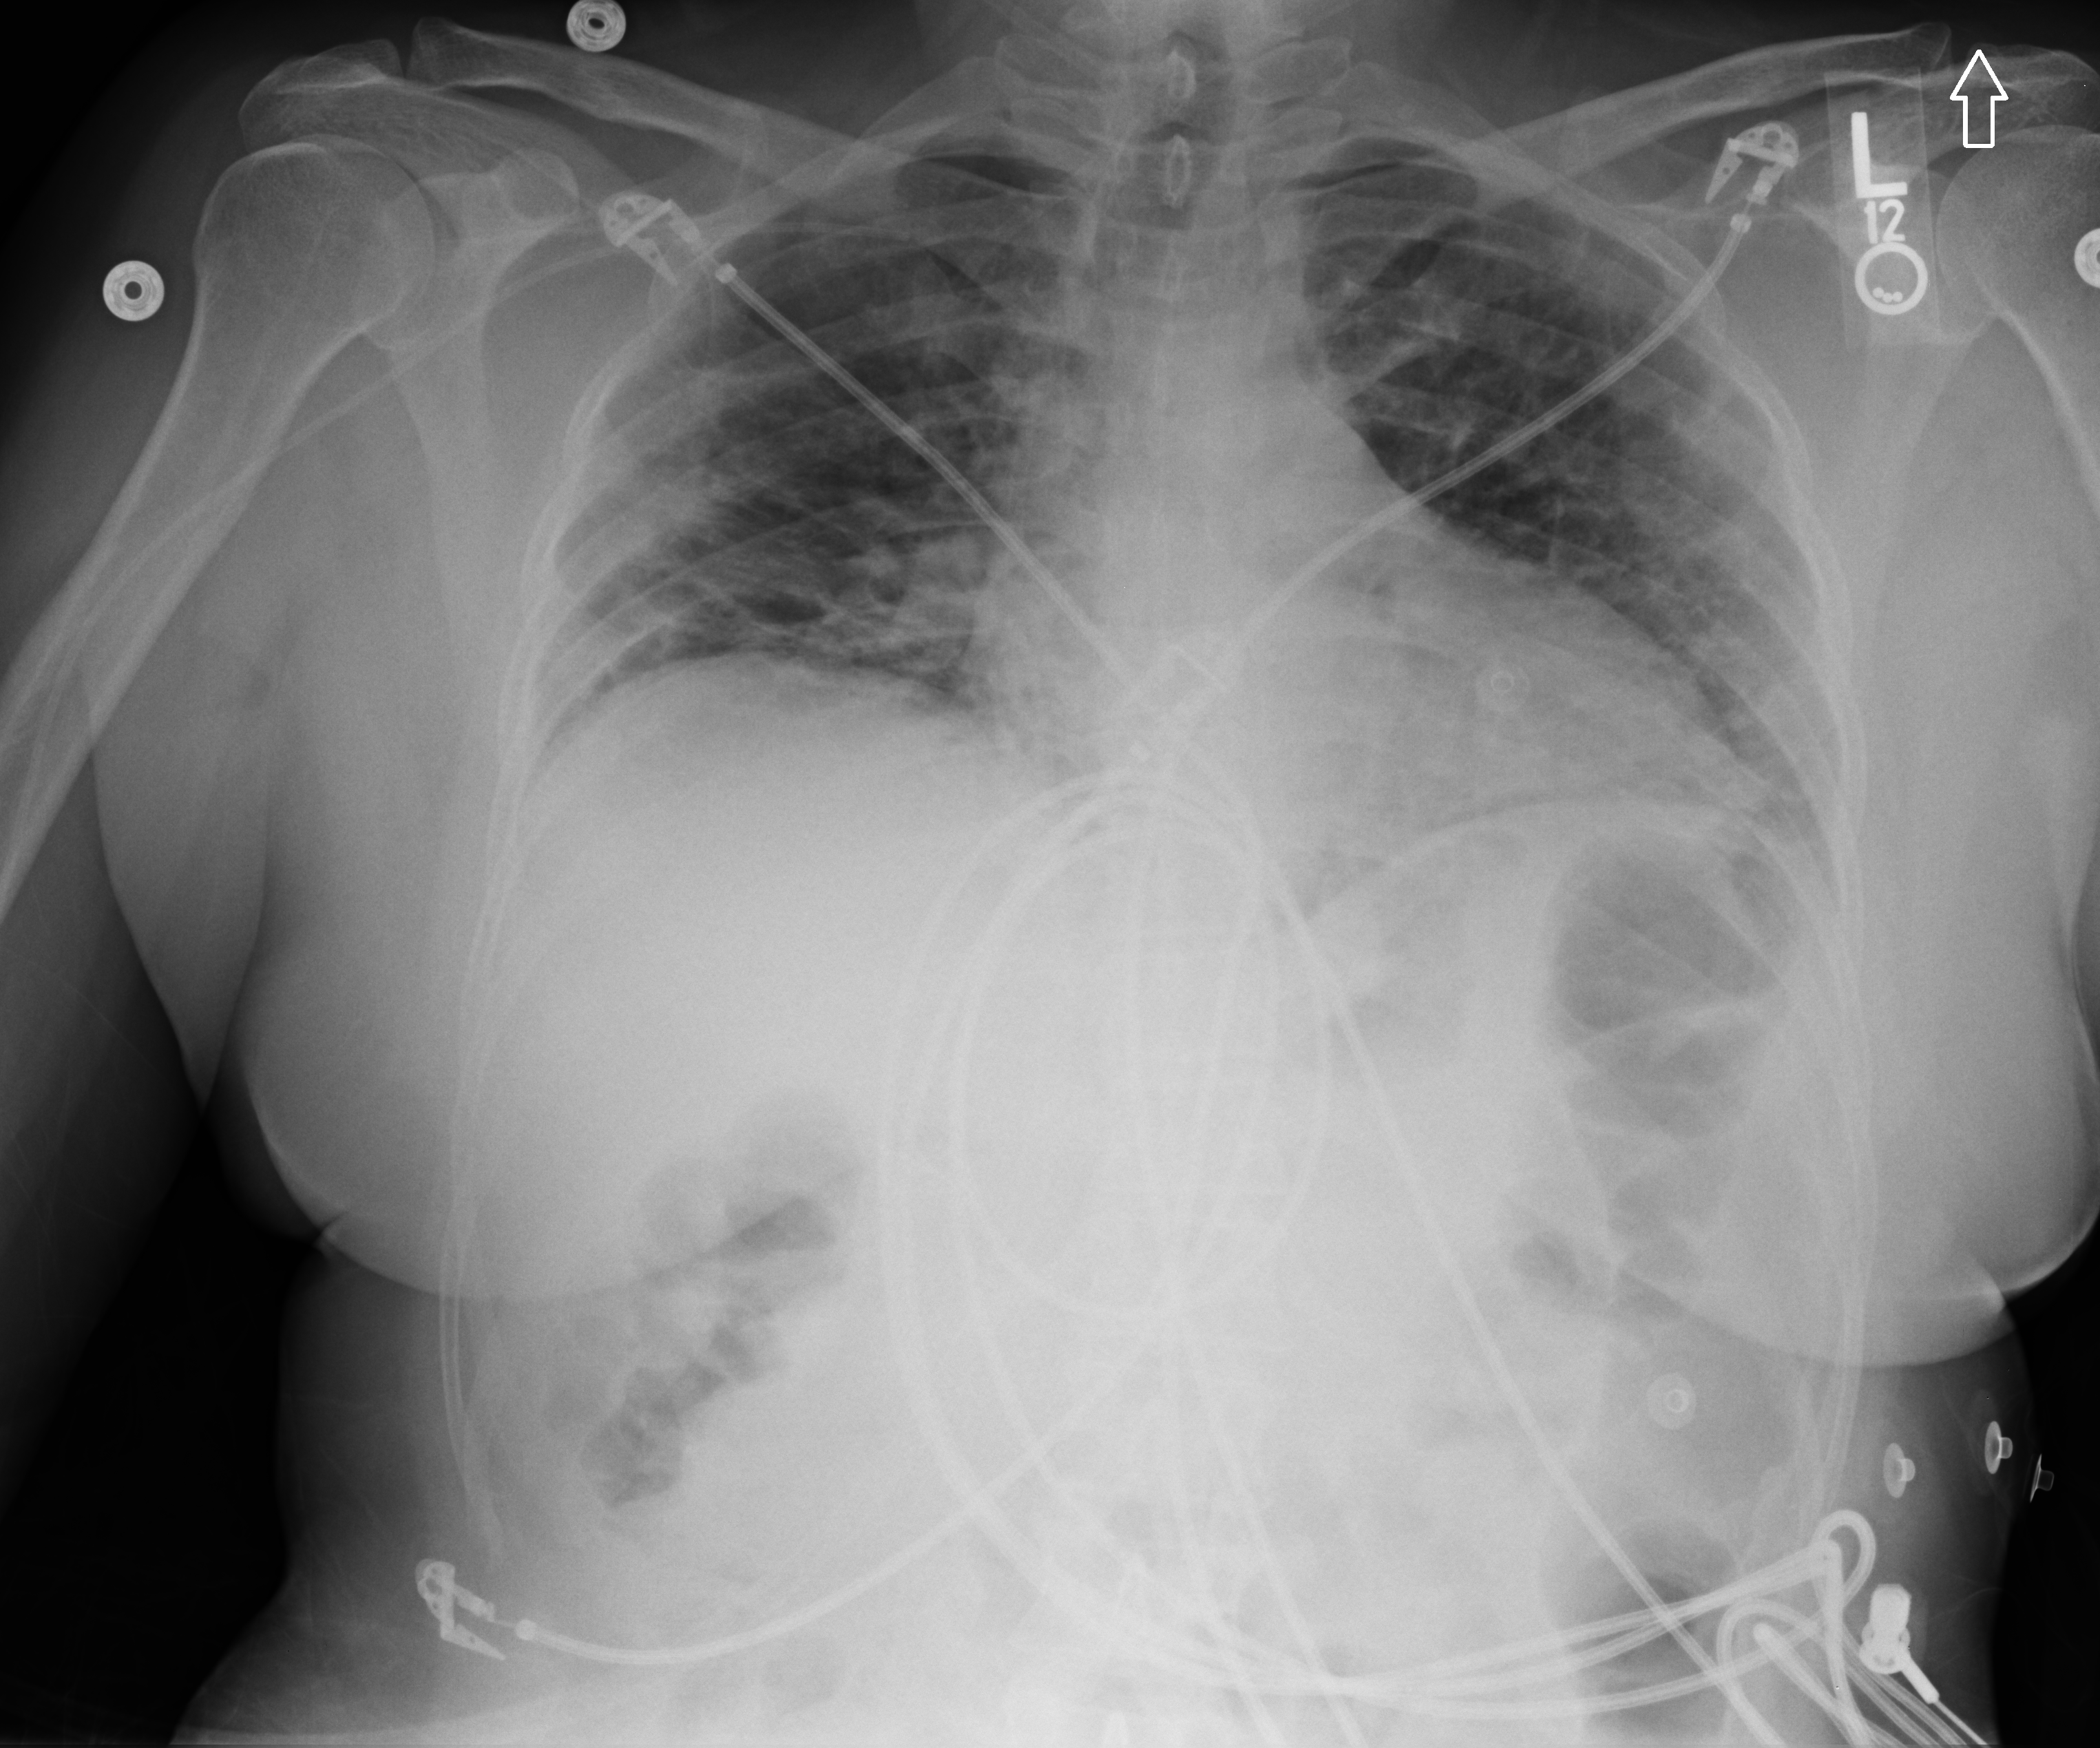
Chest X-ray (portable); anteroposterior (AP) projection. Patient hospitalised with COVID-19; female, aged 18–59 years.
Hospital-stay facts (about this admission, not read from this image; timing relative to this image not recorded): mechanically ventilated during this hospital stay: yes; COPD (admission record): no; diabetes (admission record): no.